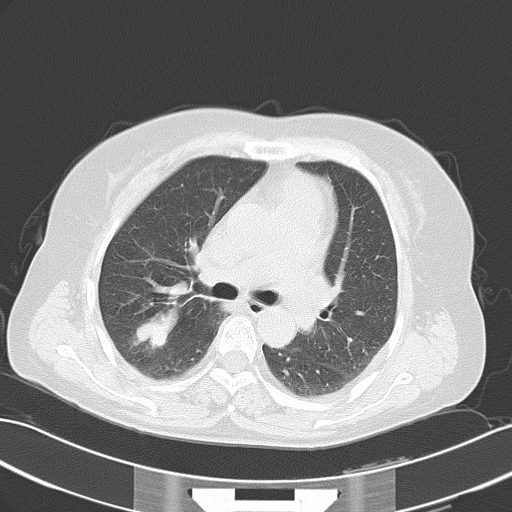
Chest CT, one axial slice. Reconstruction kernel B70f. Lung window (W 1500 / L -600 HU). 5 mm slice thickness. 512 × 512 image matrix, field of view 353 × 353 mm. Female patient, age 52 years. From the clinical record (not read from this slice): clinical TNM (as recorded): T1c N3 M1a.
Outlined on this slice (bounding box drawn by a radiologist):
- lung tumour (recorded histology: adenocarcinoma): bounding box [x1, y1, x2, y2] px = [130, 307, 183, 353]